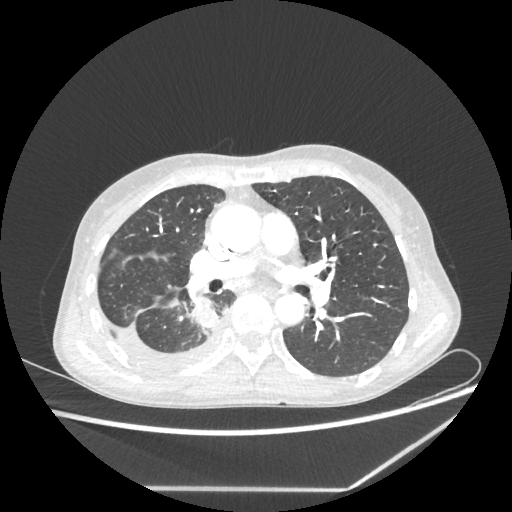
Chest CT, one axial slice; slice 130 of 237 in the series (ordered by position); reconstruction kernel STANDARD; 80 kVp; lung window (W 1500 / L -600 HU); 512 × 512 image matrix. Patient: female, 59 years. From the clinical record (not read from this slice): clinical TNM (as recorded): T1c N1 M1.
Outlined on this slice (bounding box drawn by a radiologist):
- lung tumour (recorded histology: adenocarcinoma): box from (x=191, y=300) to (x=218, y=331) px